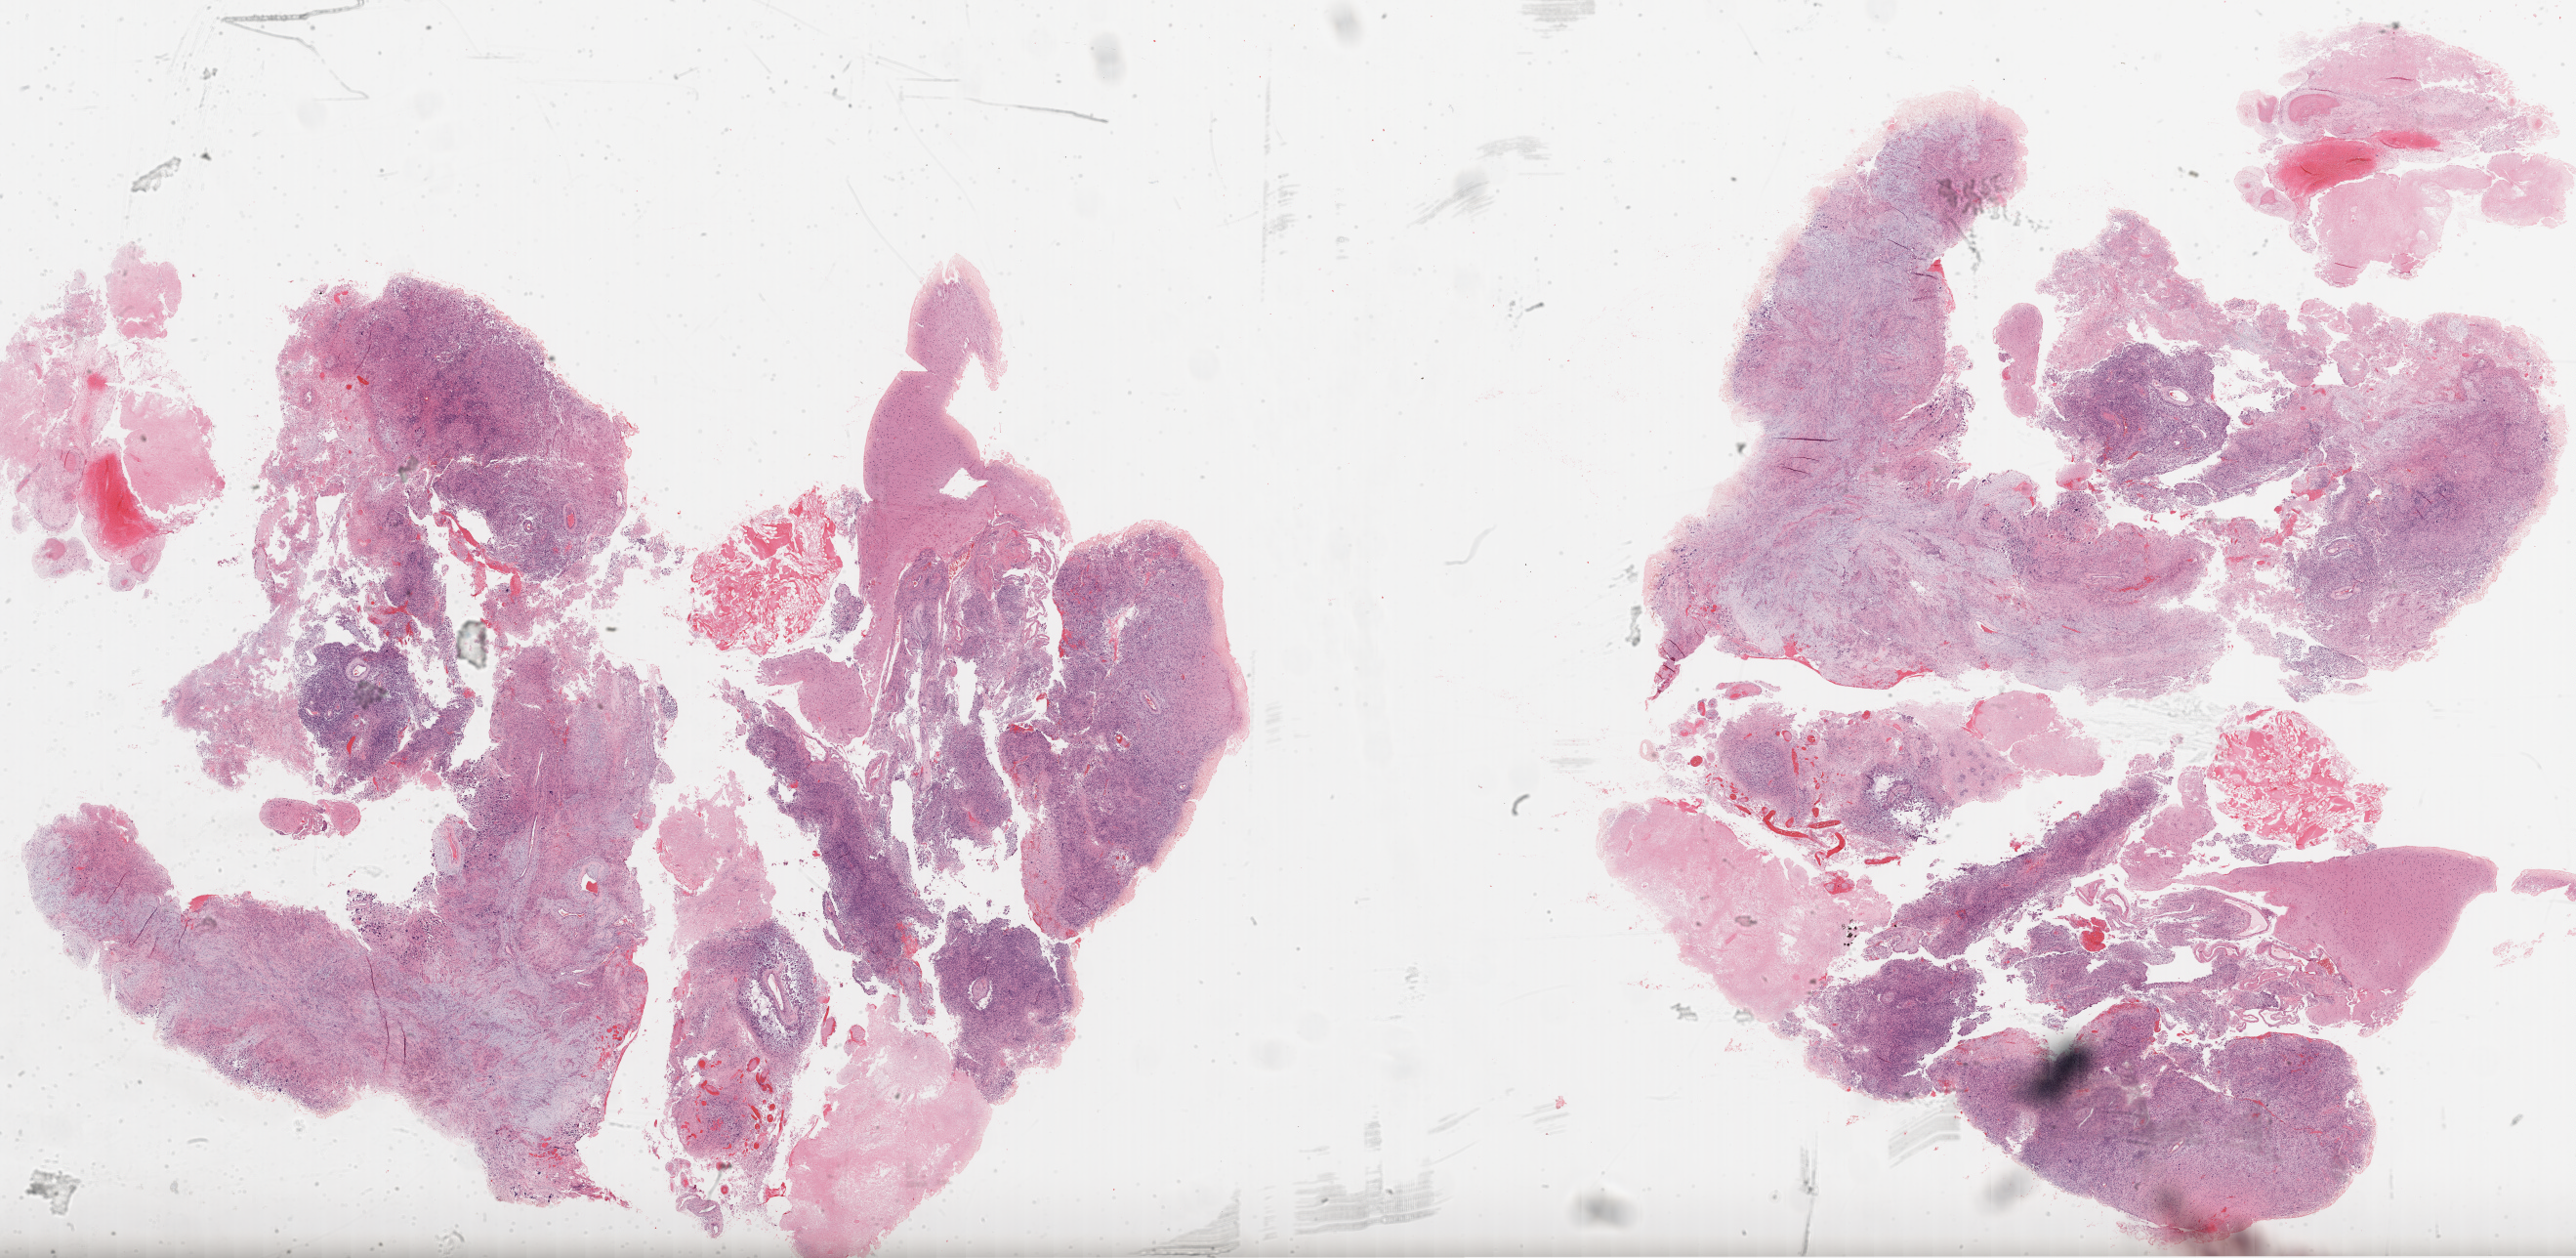
Whole-slide histology image, H&E-stained — low-resolution overview of the scanned area, about 42.5 x 20.8 mm, formalin-fixed paraffin-embedded (FFPE) diagnostic section, brain, primary tumour sample. Patient: male, age at initial diagnosis 67 years.
Diagnosis: Glioblastoma.